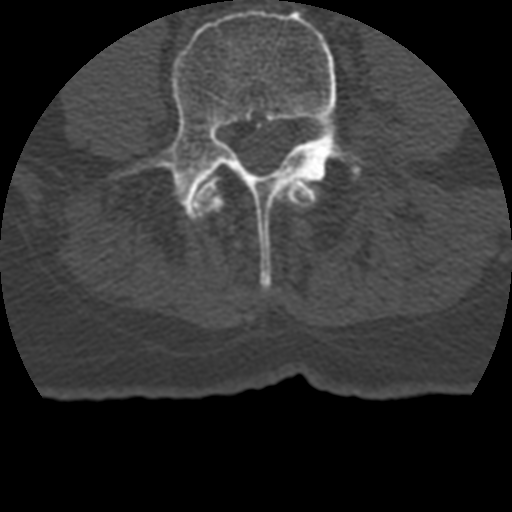
CT including the spine, one axial slice; slice 68 of 399 in the series (ordered by position); reconstruction kernel STANDARD; 120 kVp; bone window (W 1800 / L 400 HU); 1.25 mm slice thickness; 512 × 512 image matrix. Patient age 69 years. Case-level facts recorded for this patient, not image findings: primary cancer: prostate.
Annotated regions visible in this slice (semi-automatically segmented with operator editing):
- L3 vertebra: bounding box (x1, y1, x2, y2) in pixels: (194, 179, 317, 214)
- L4 vertebra: (113, 9, 361, 293)
- L5 vertebra: (350, 165, 361, 176)